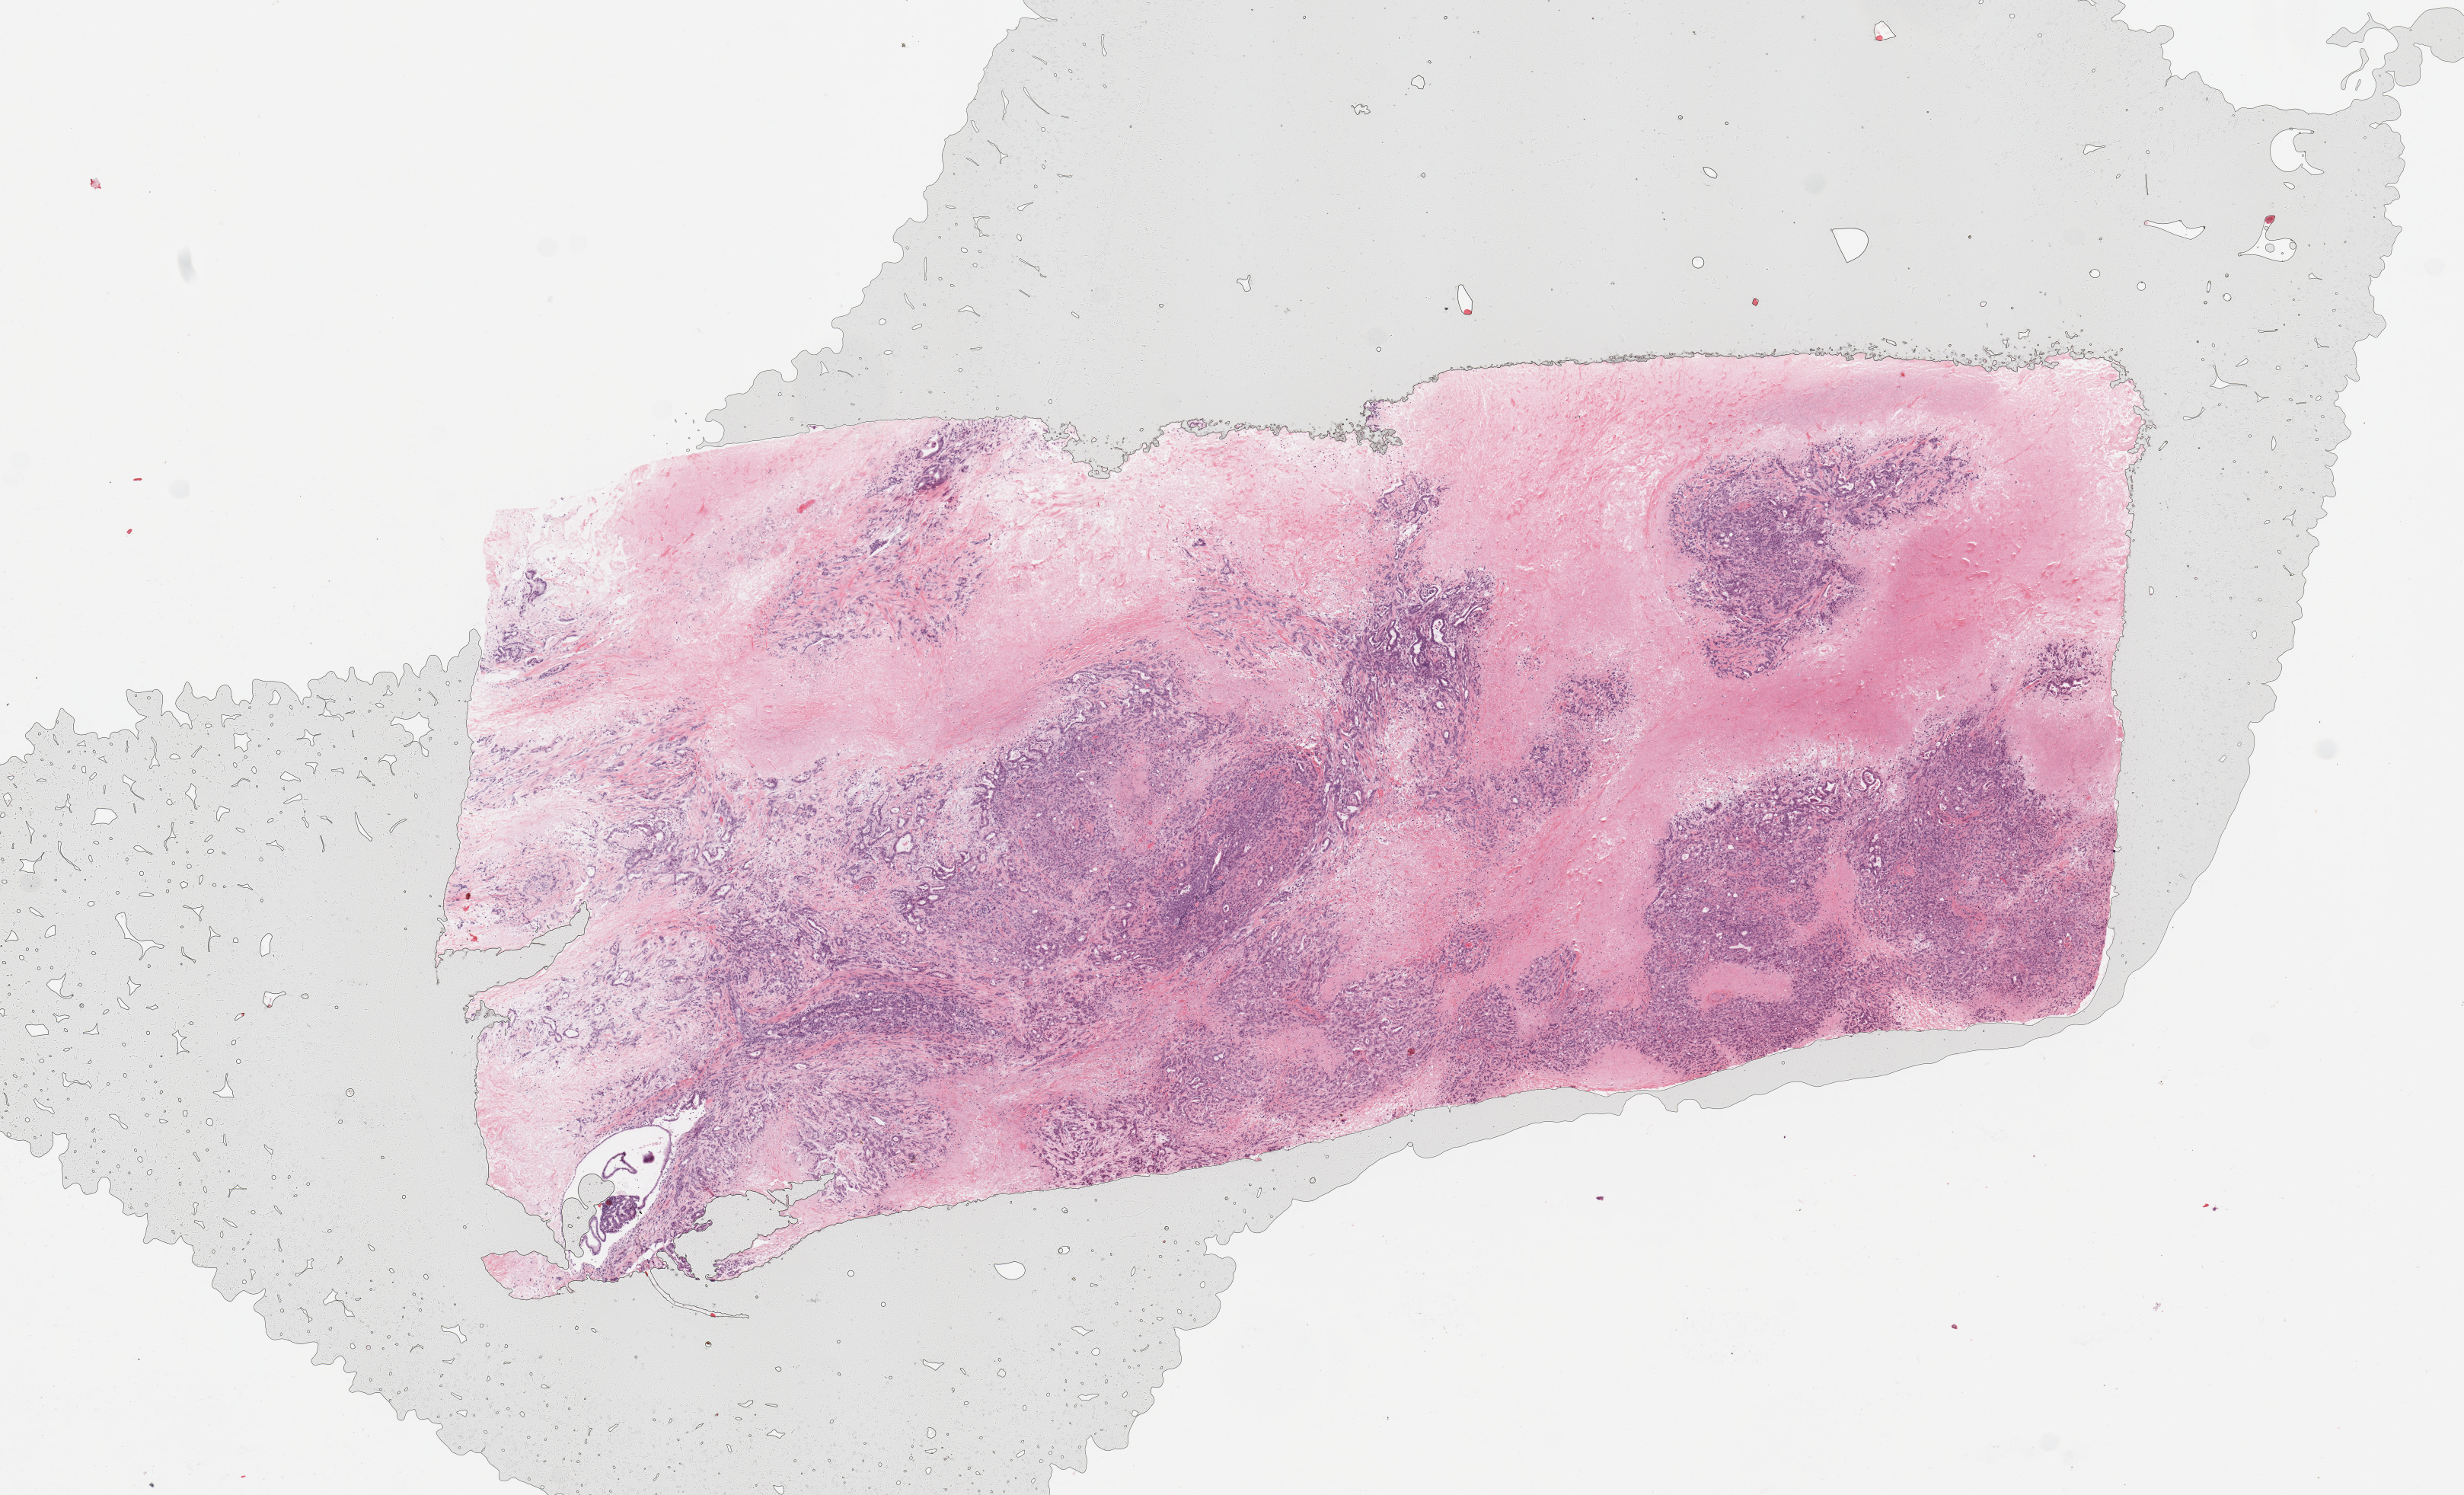
H&E-stained whole-slide image, a low-resolution overview of the entire scanned area, about 12.8 x 7.8 mm; tumour tissue sample, pancreas. Female, 50 y/o. Histologic grade: G2 (moderately differentiated).
Primary tumour site (as recorded): body. AJCC pathologic stage: III. Diagnosis: Infiltrating duct carcinoma, NOS.